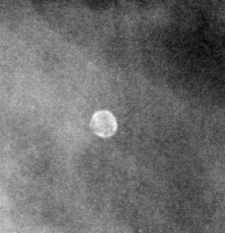
Cropped region of a digitized screen-film mammogram centred on a radiologist-marked abnormality, left breast, MLO view.
Marked abnormality: calcifications, morphology lucent center; BI-RADS assessment category 2; subtlety rating 3 on a 1 (subtle) to 5 (obvious) scale; benign without callback (not worked up further).